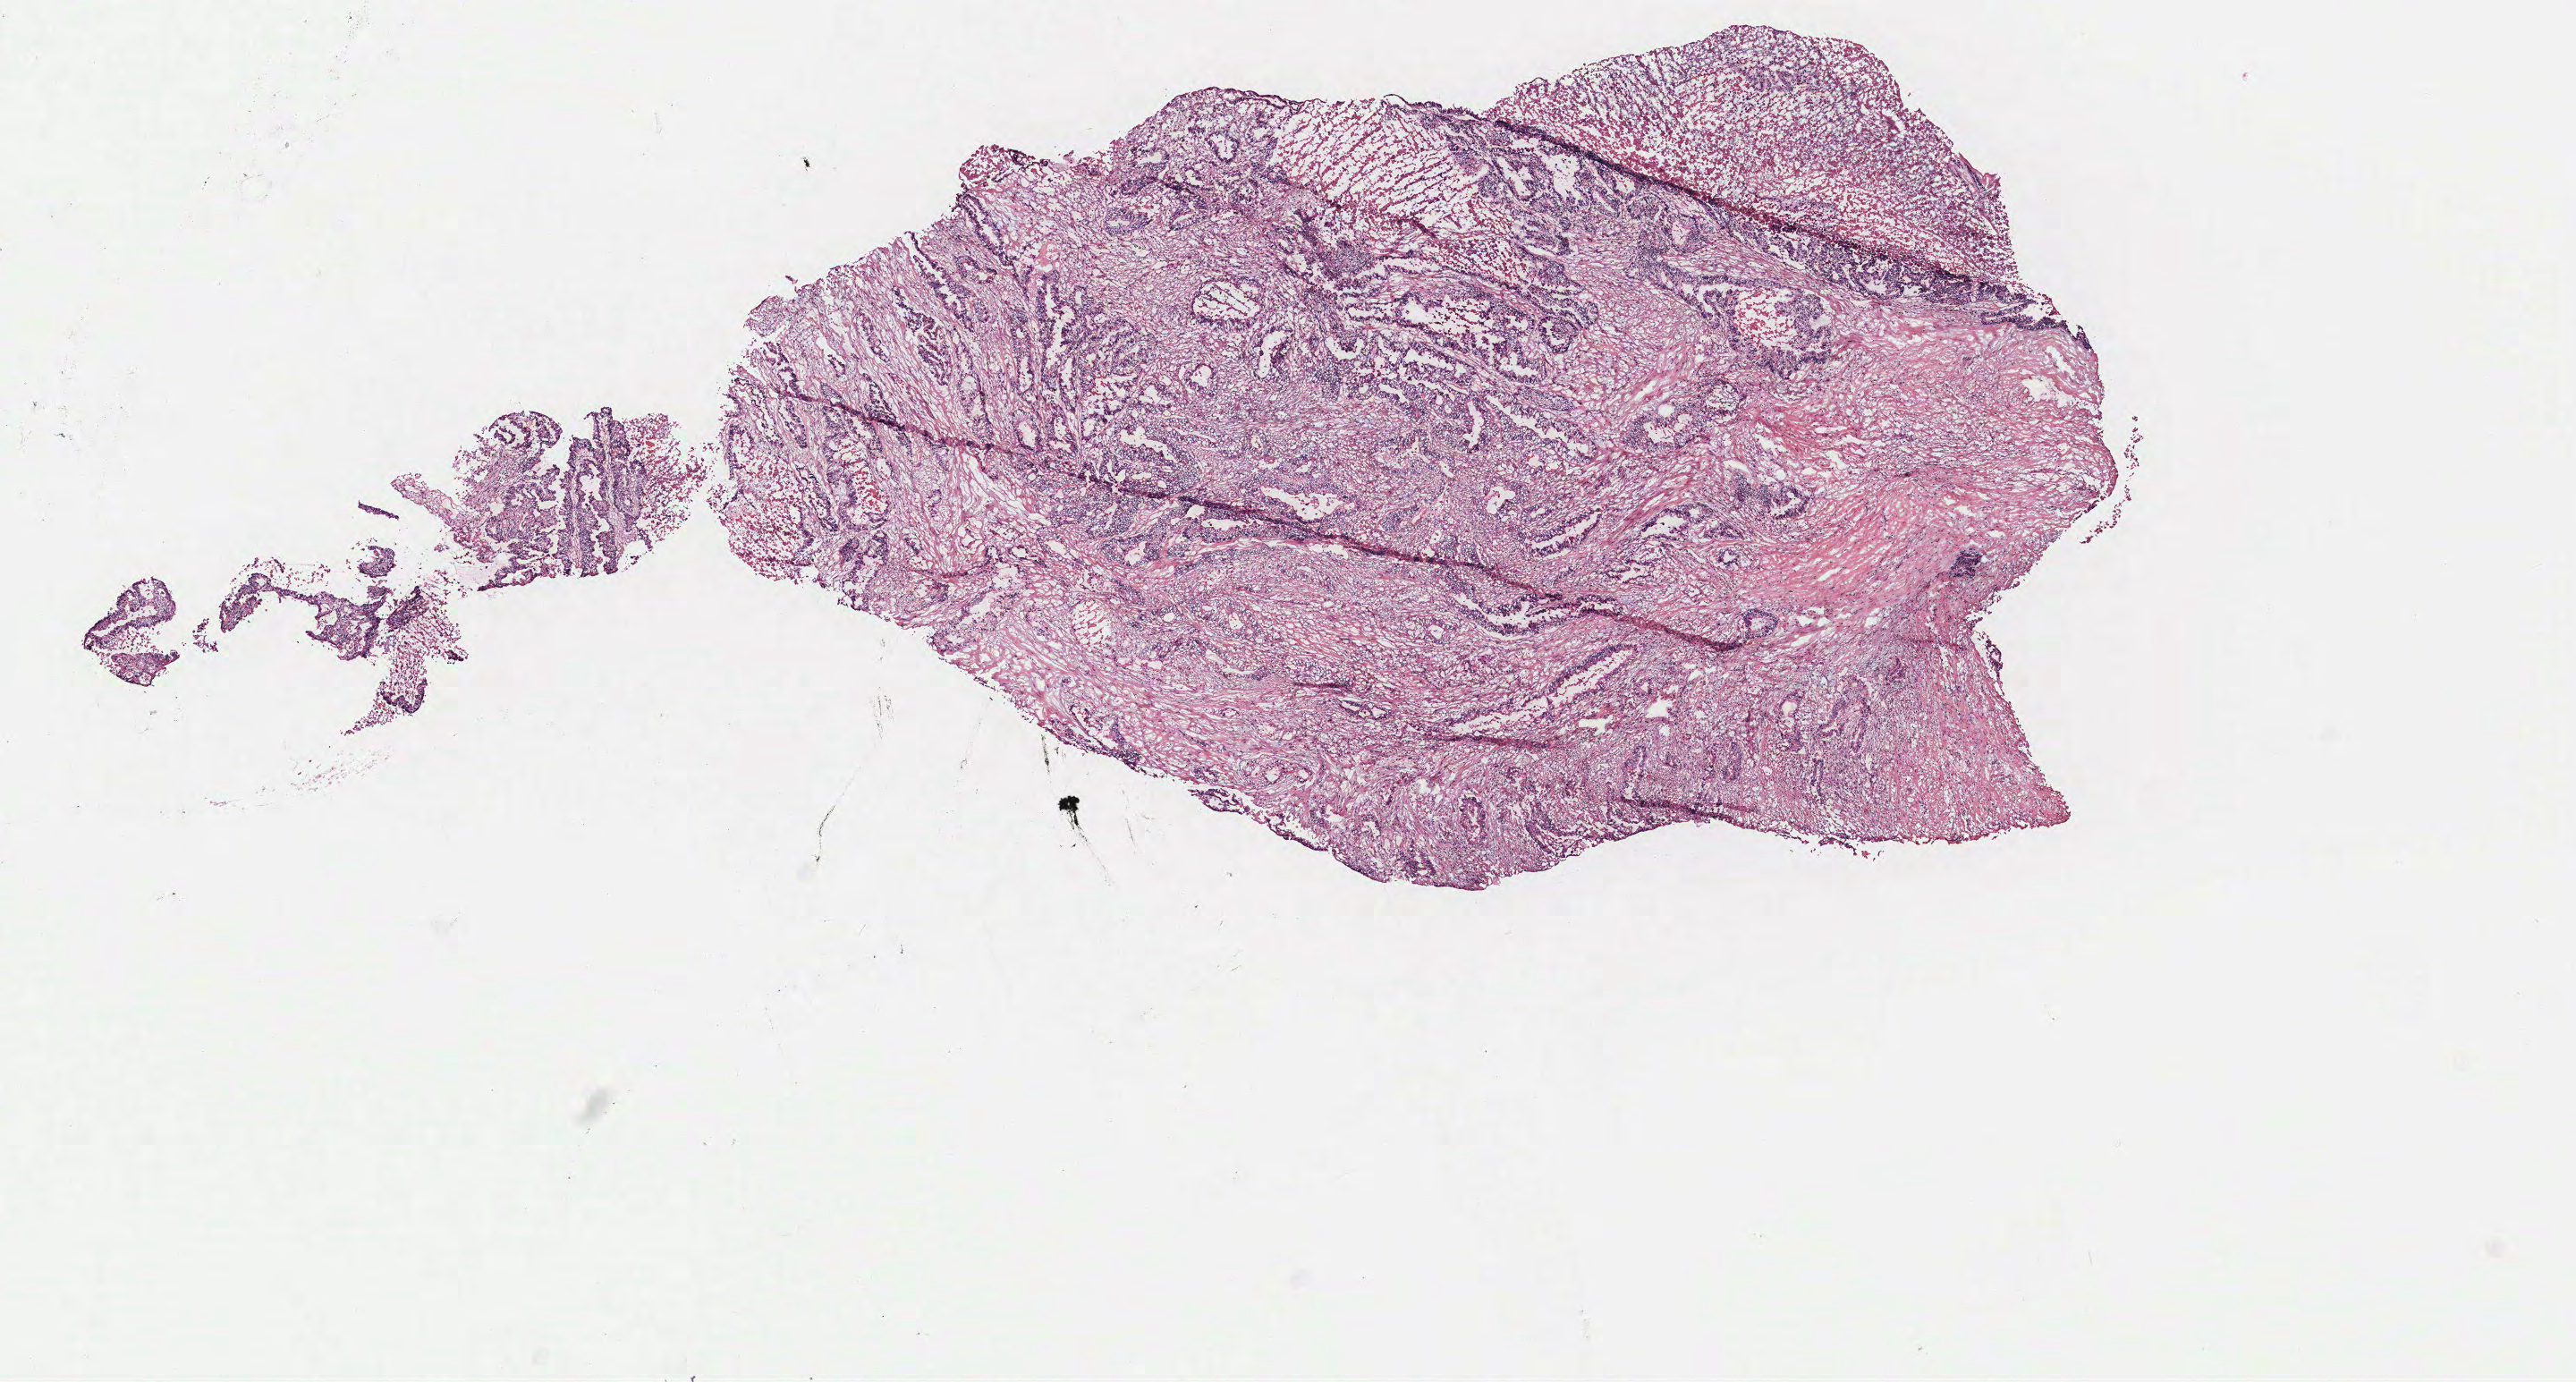
Digitized H&E tissue section (whole slide) — low-resolution overview of the scanned area, about 11.5 x 6.2 mm (acquisition: 40x scan); colon, tissue type not recorded.
- patient diagnosis (cohort enrolment): colon cancer (colon)